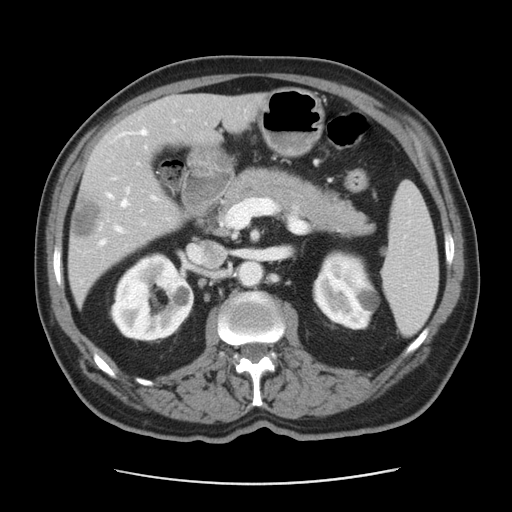
Contrast-enhanced abdominal CT, one axial slice; reconstruction kernel STANDARD; soft-tissue window (W 400 / L 40 HU); 5 mm slice thickness; 512 × 512 image matrix, field of view 370 × 370 mm. Male patient, age 73 years. From the clinical record (not read from this slice): diagnosis: colorectal cancer liver metastases, imaged before liver resection; multiple liver metastases: yes; largest metastasis: 0.5 cm.
Outlined on this slice (expert manual segmentation):
- hepatic veins: box from (x=98, y=130) to (x=146, y=246) px
- liver: (x=70, y=94)–(x=264, y=302)
- planned liver remnant (the part of the liver to remain after resection): (x=110, y=94)–(x=264, y=167)
- portal vein (with intrahepatic branches): (x=115, y=226)–(x=122, y=232)
- liver metastasis: (x=73, y=200)–(x=101, y=238)